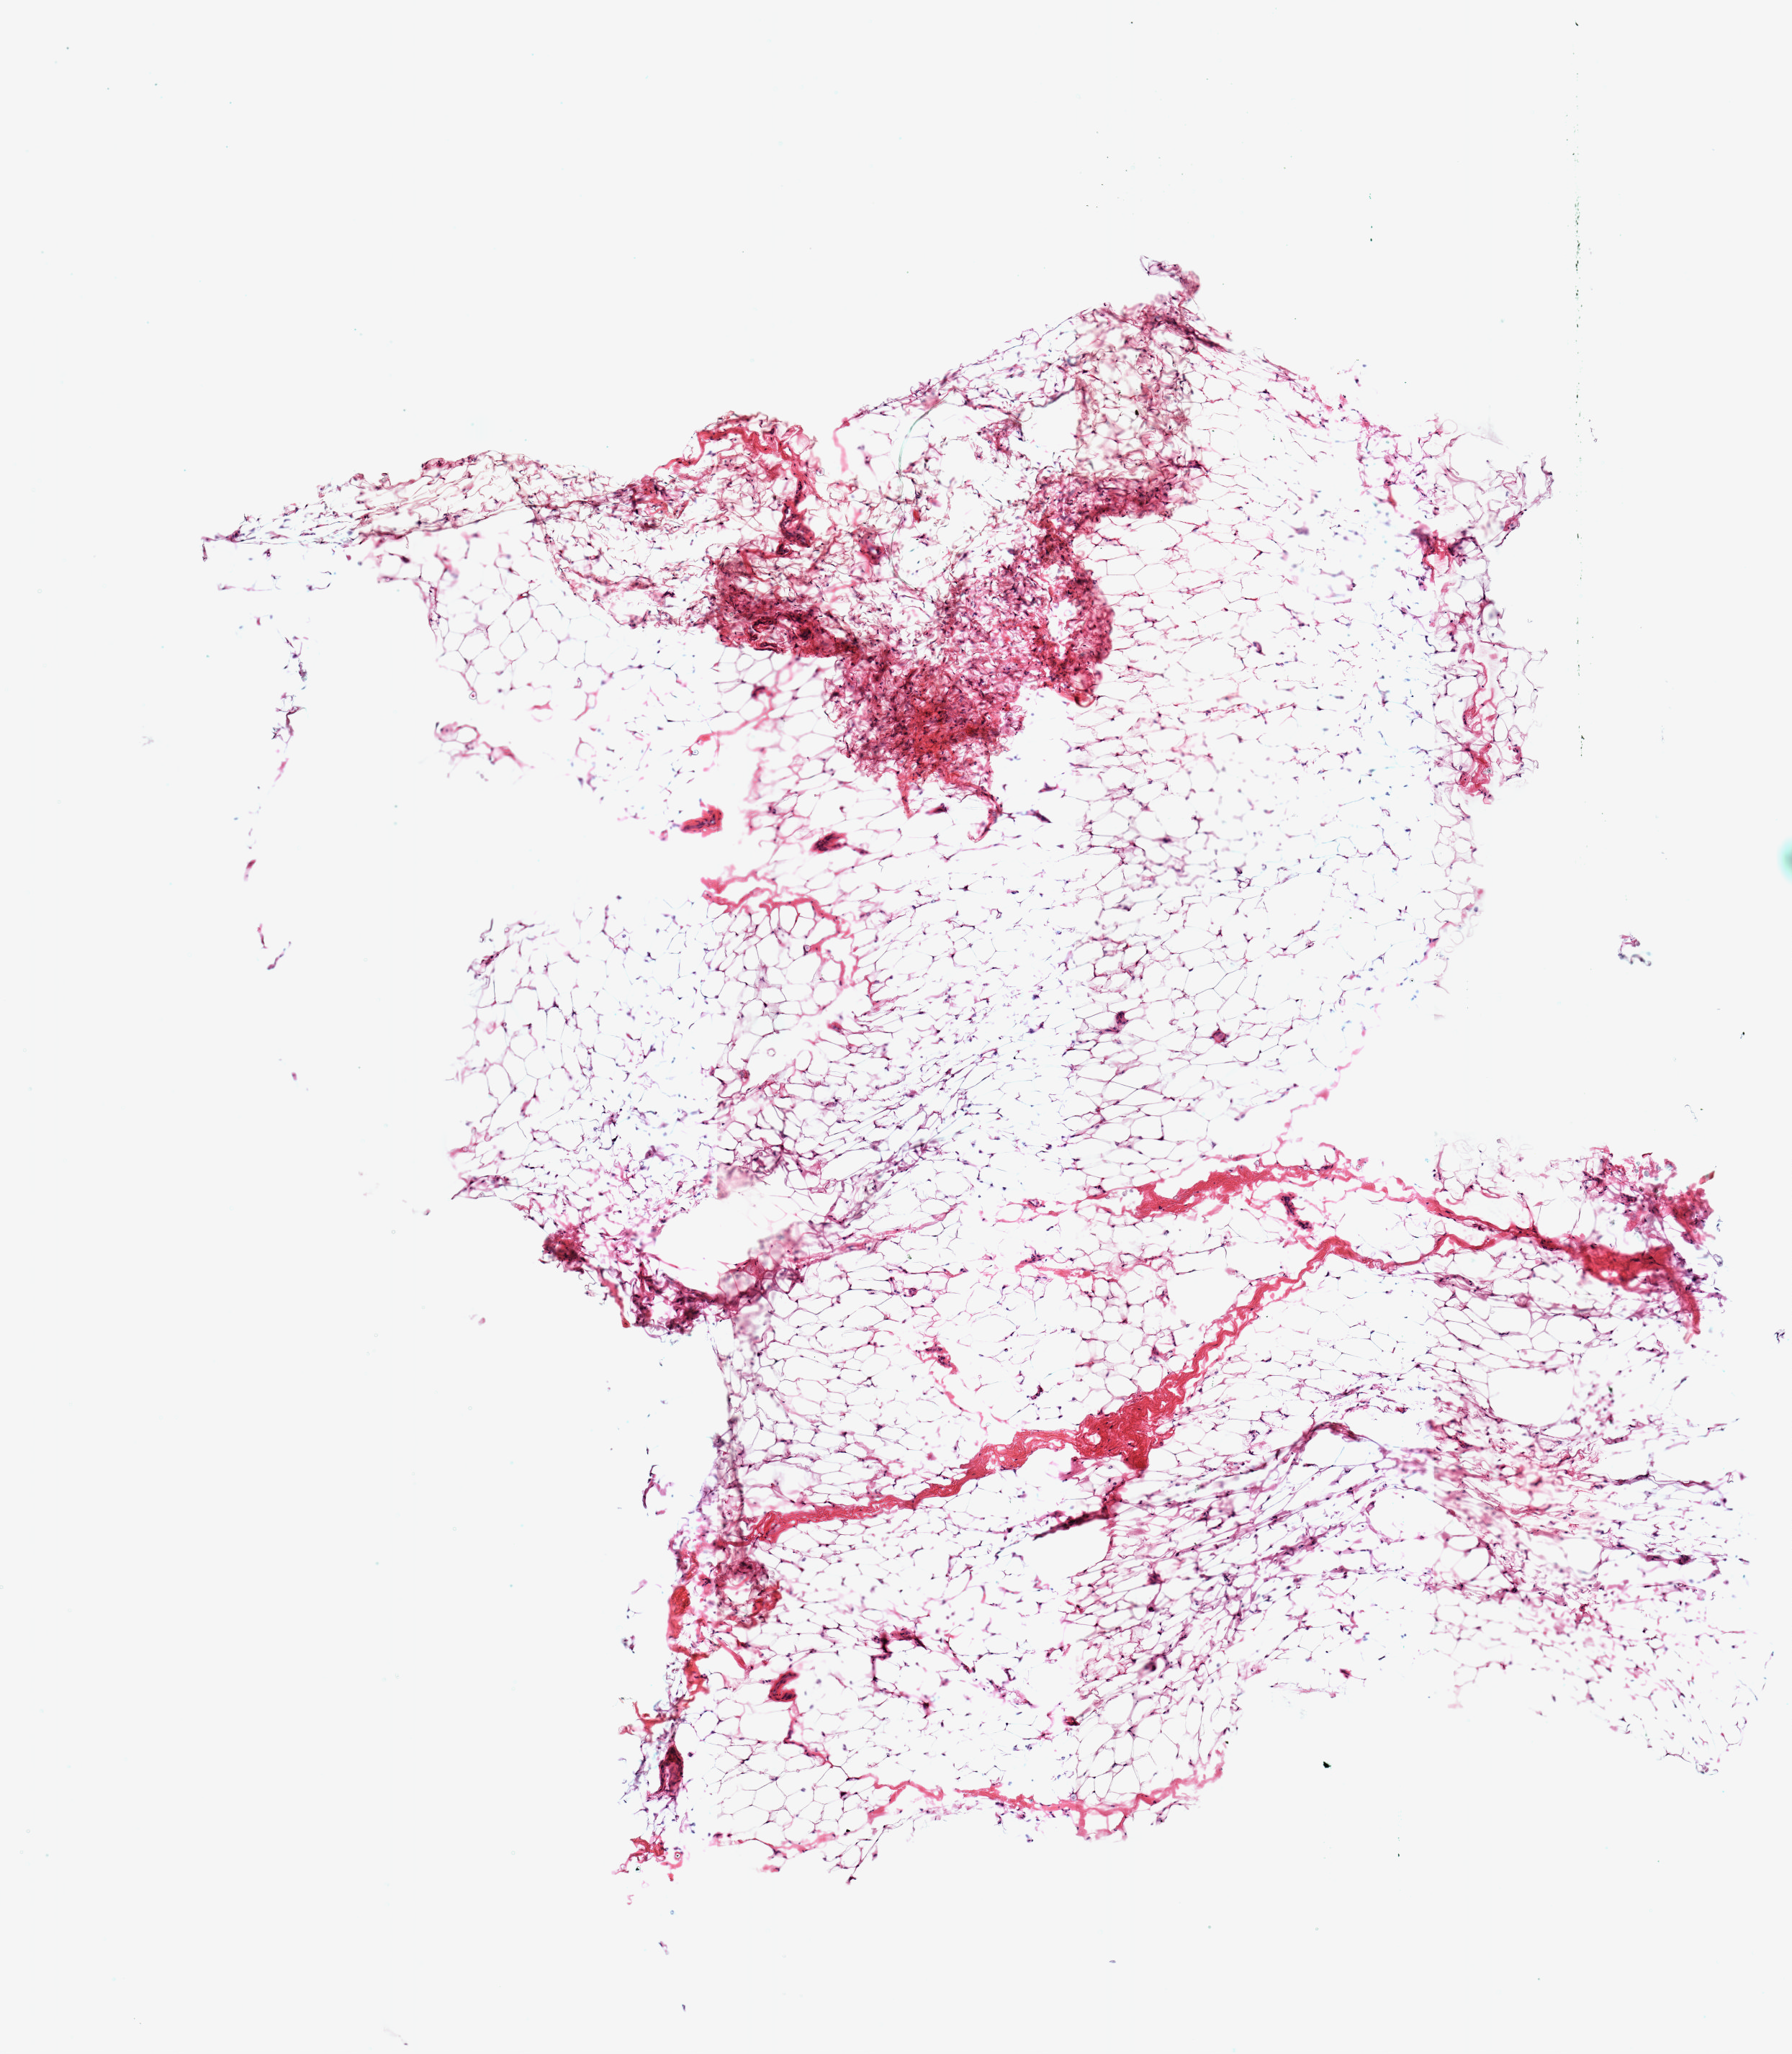
Whole-slide image, hematoxylin and eosin (H&E) stain — a low-resolution overview of the entire scanned area, about 4.9 x 5.6 mm (slide scanned at 20x). Frozen section. Section of breast (target tissue). Donor tissue sample. Donor sex: female.
• pathologist's review note for this sample: 1 piece